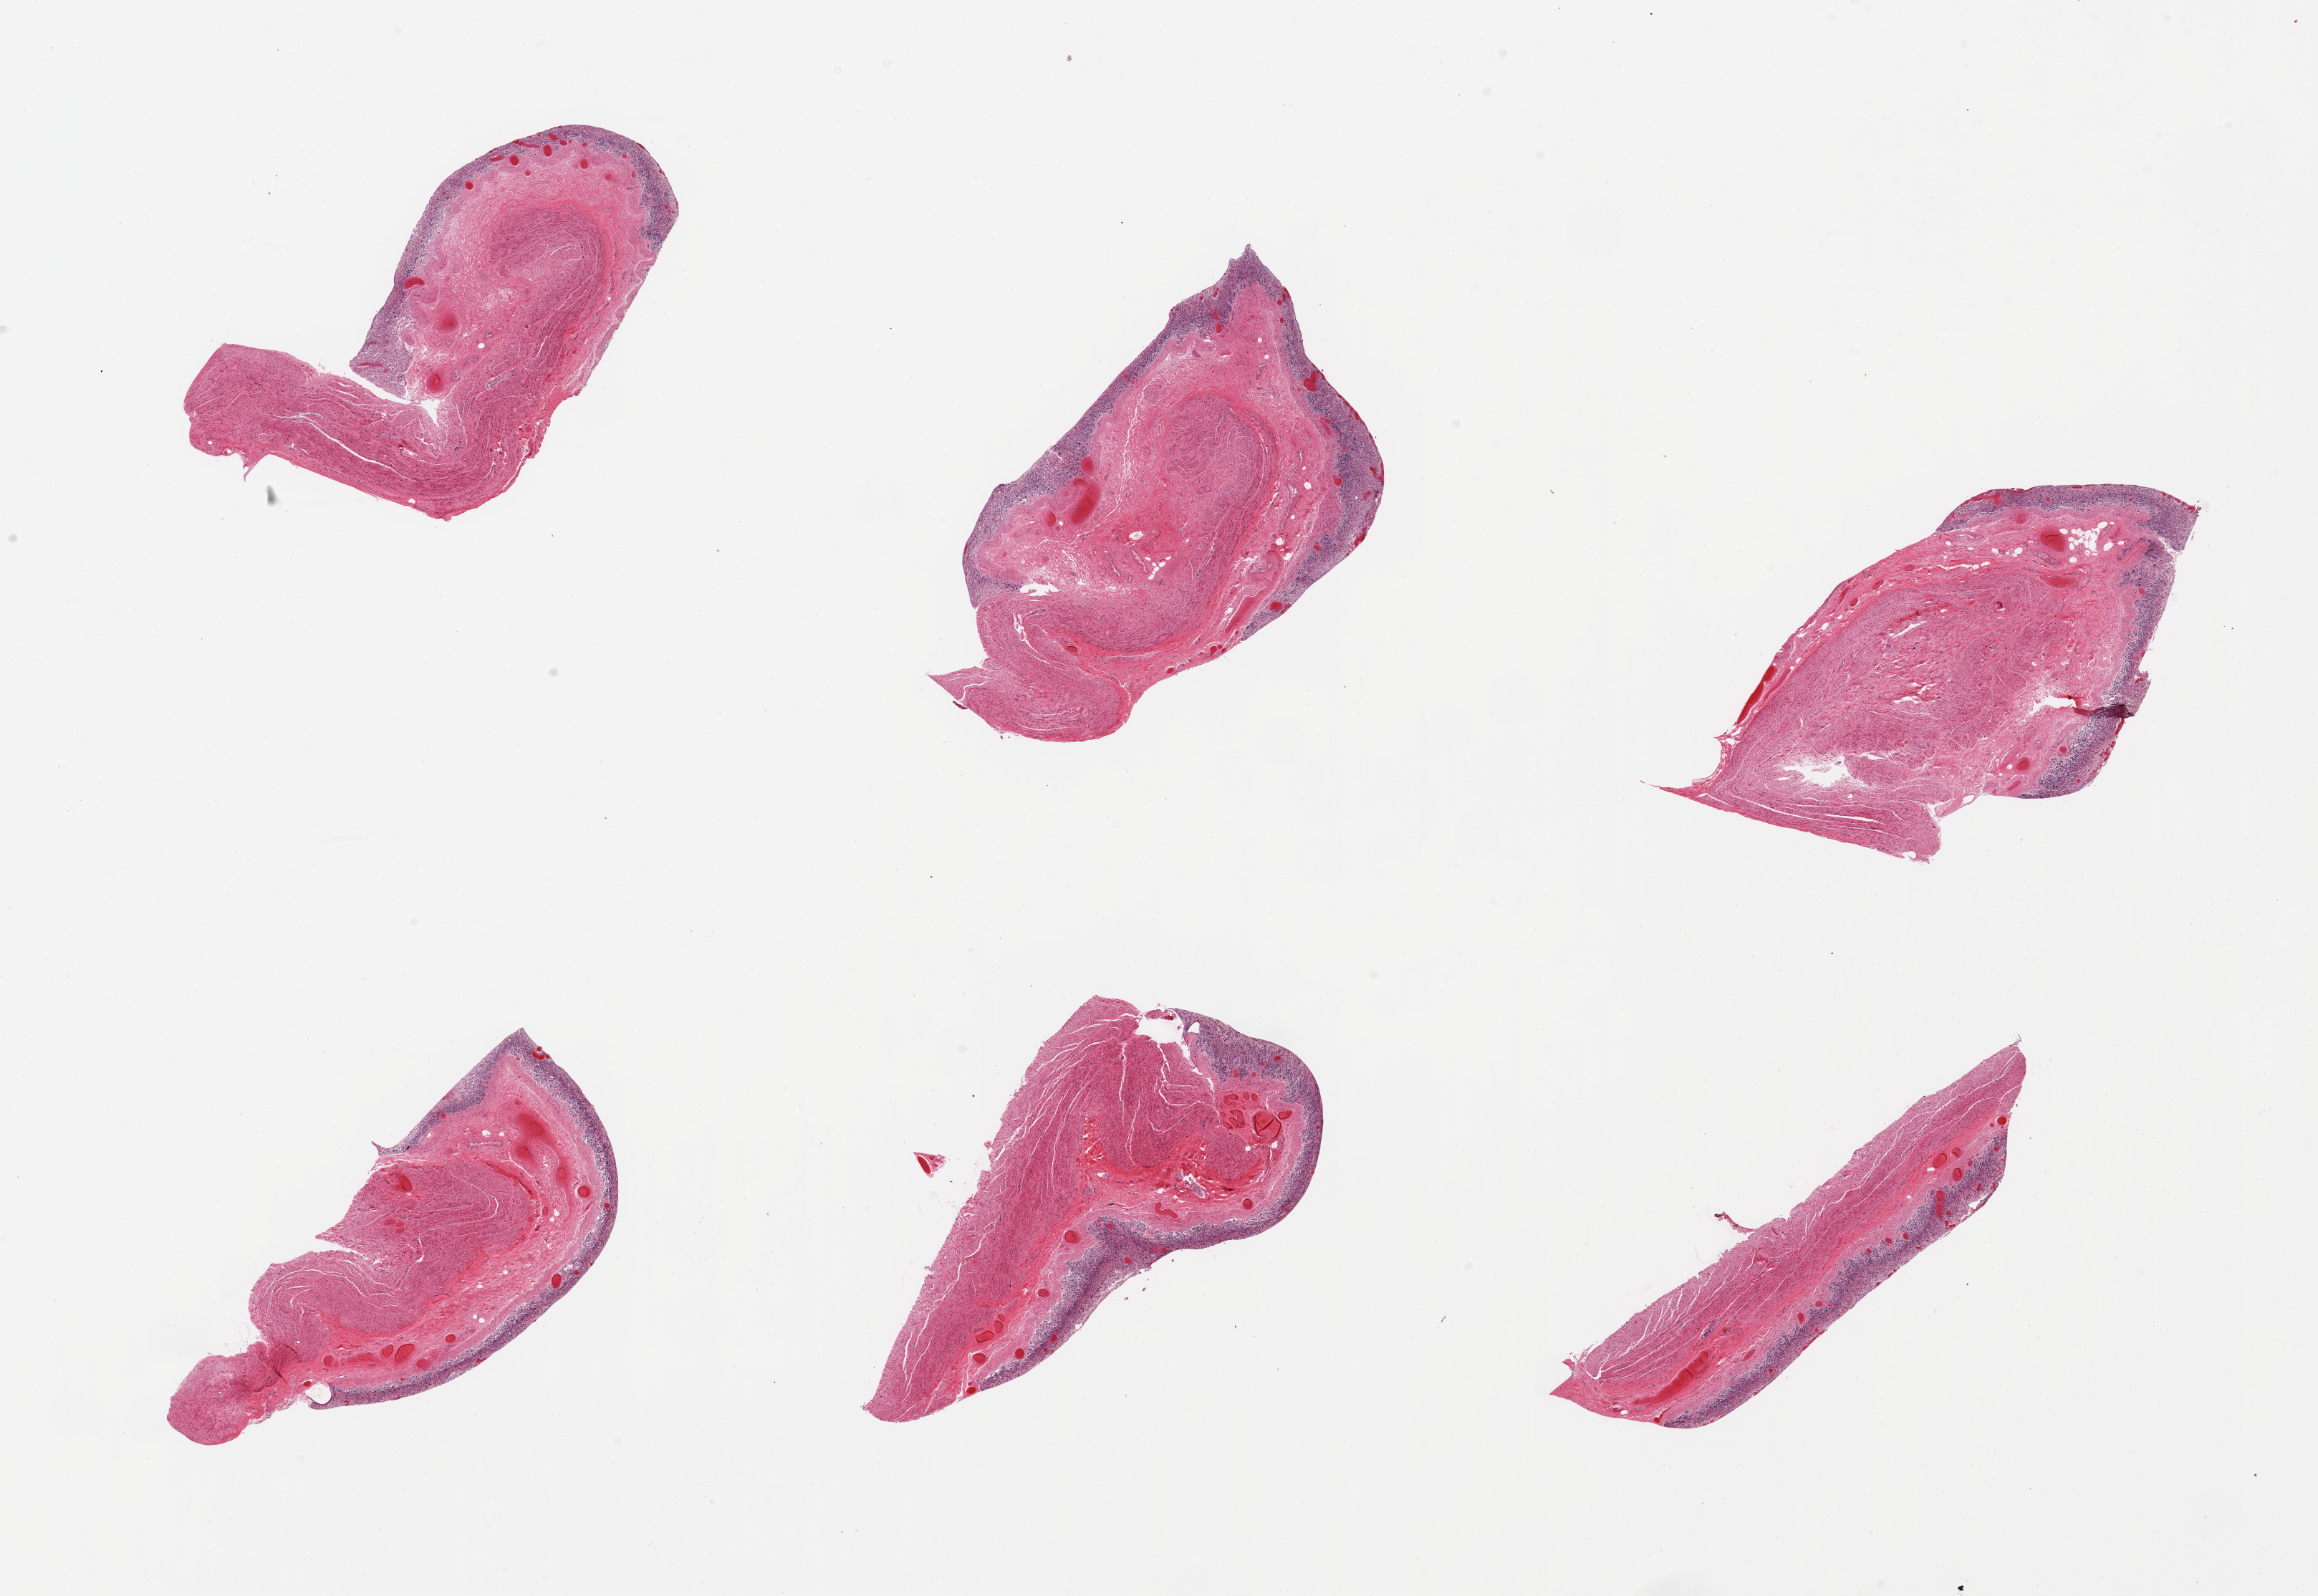
Haematoxylin and eosin whole-slide image, low-resolution overview of the scanned area, about 25.6 x 17.6 mm. PAXgene-fixed paraffin-embedded (PFPE) section. Section of stomach (target tissue). Donor tissue sample. Donor sex: female.
- pathologist's review note for this sample: 6 pieces; mucosa totally autolyzed, muscularis intact